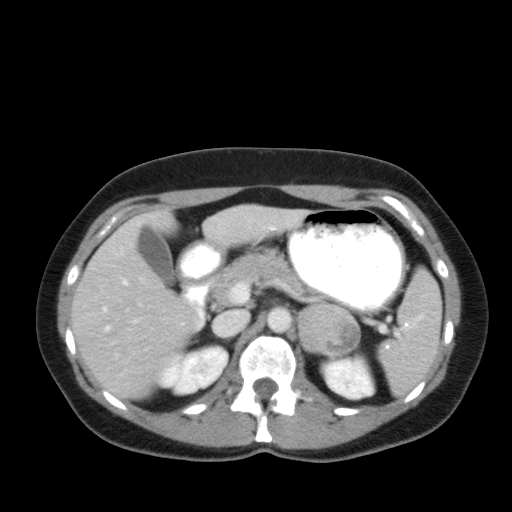
Contrast-enhanced abdominal CT, one axial slice. Position 33 of 92 along the scan axis. Reconstruction kernel FC12. 120 kVp. Soft-tissue window (W 400 / L 40 HU). 512 × 512 image matrix, field of view 369 × 369 mm. Female patient, age 35 years. Case-level facts recorded for this patient, not image findings: diagnosis: adrenocortical carcinoma; tumour side: left adrenal; tumour size at pathology: 6.6 cm; Ki-67 index: 5 %; stage (as recorded): 2.
Outlined on this slice (semi-automatic segmentation, software-assisted and operator-edited):
- mass: bounding box [x1, y1, x2, y2] px = [299, 305, 358, 356]